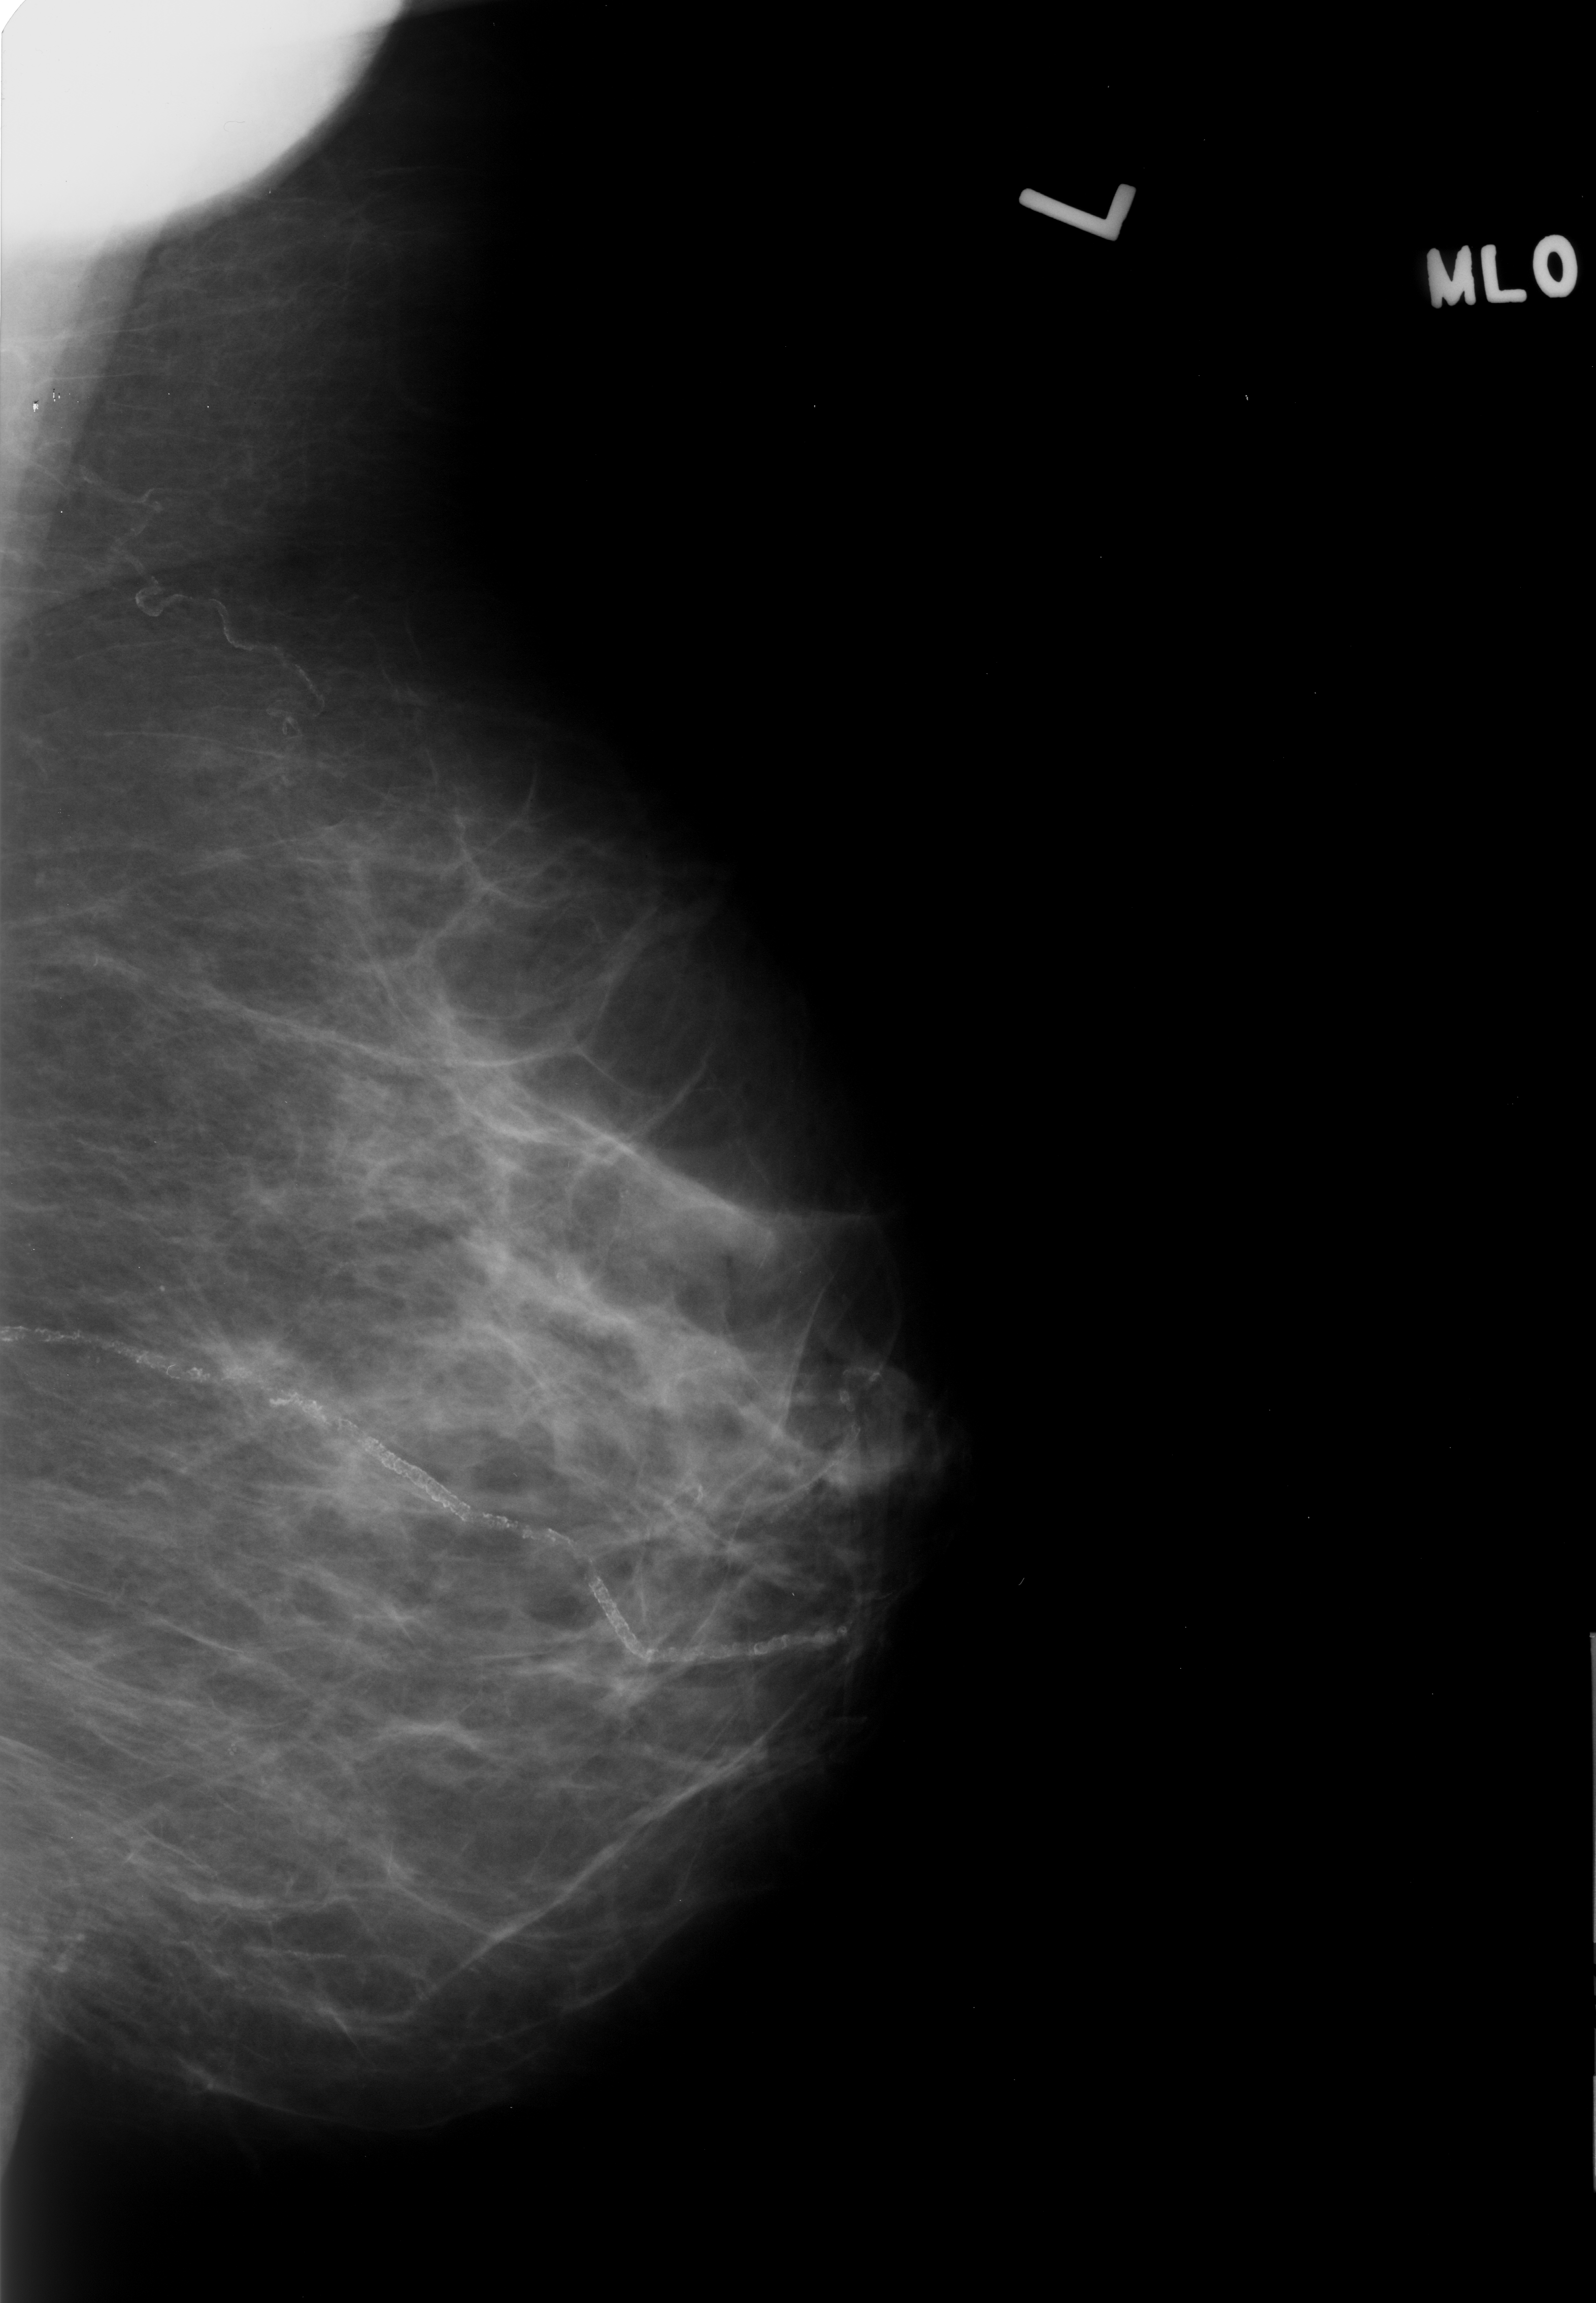
Digitized screen-film mammogram; left breast; MLO view; breast composition: scattered fibroglandular densities (BI-RADS density category 2 of 4); 1596 × 2303 image matrix.
Expert-marked regions of interest on this film, with their recorded descriptors:
- Finding 1 of 2: calcifications, morphology pleomorphic, distribution clustered; BI-RADS assessment category 4; subtlety rating 2 on a 1 (subtle) to 5 (obvious) scale; pathology (as recorded): benign: box from (x=536, y=1263) to (x=610, y=1329) px
- Finding 2 of 2: calcifications, morphology pleomorphic, distribution clustered; BI-RADS assessment category 4; pathology result (as recorded, not read from the image): benign: (x=670, y=1263)–(x=752, y=1341)